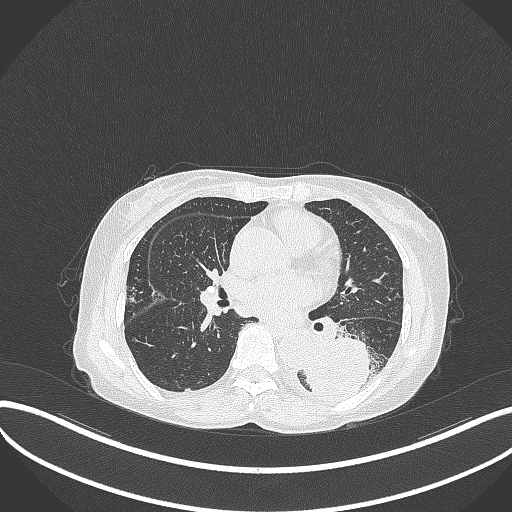
Chest CT, one axial slice; slice 154 of 370 in the series (ordered by position); reconstruction kernel B70f; 120 kVp; lung window (W 1500 / L -600 HU); 1 mm slice thickness; 512 × 512 image matrix. Female patient, age 78 years. Case-level facts recorded for this patient, not image findings: clinical TNM (as recorded): T3 N0 M1.
Structures marked on this image (rectangle marked by the reading radiologist):
- lung tumour (recorded histology: squamous cell carcinoma): bounding box [x1, y1, x2, y2] px = [304, 329, 390, 403]